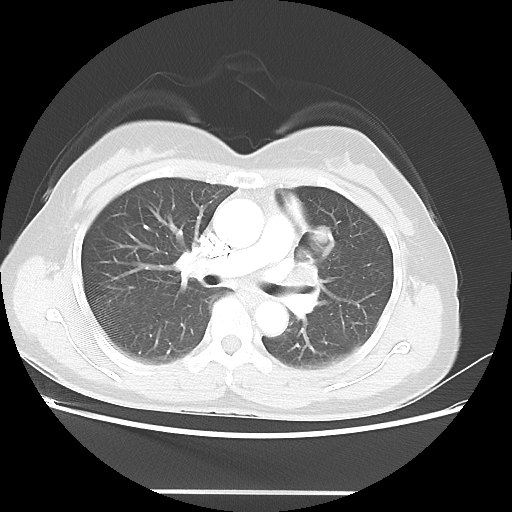
Chest CT, one axial slice; slice 27 of 46 in the series (ordered by position); reconstruction kernel LUNG; 100 kVp; lung window (W 1500 / L -600 HU); 5 mm slice thickness; 512 × 512 image matrix. Patient: female, 50 years. From the clinical record (not read from this slice): clinical TNM (as recorded): T1c N1 M0; histopathological grade: G3.
Outlined on this slice (bounding box drawn by a radiologist):
- lung tumour (recorded histology: adenocarcinoma): bounding box [x1, y1, x2, y2] px = [312, 222, 334, 258]